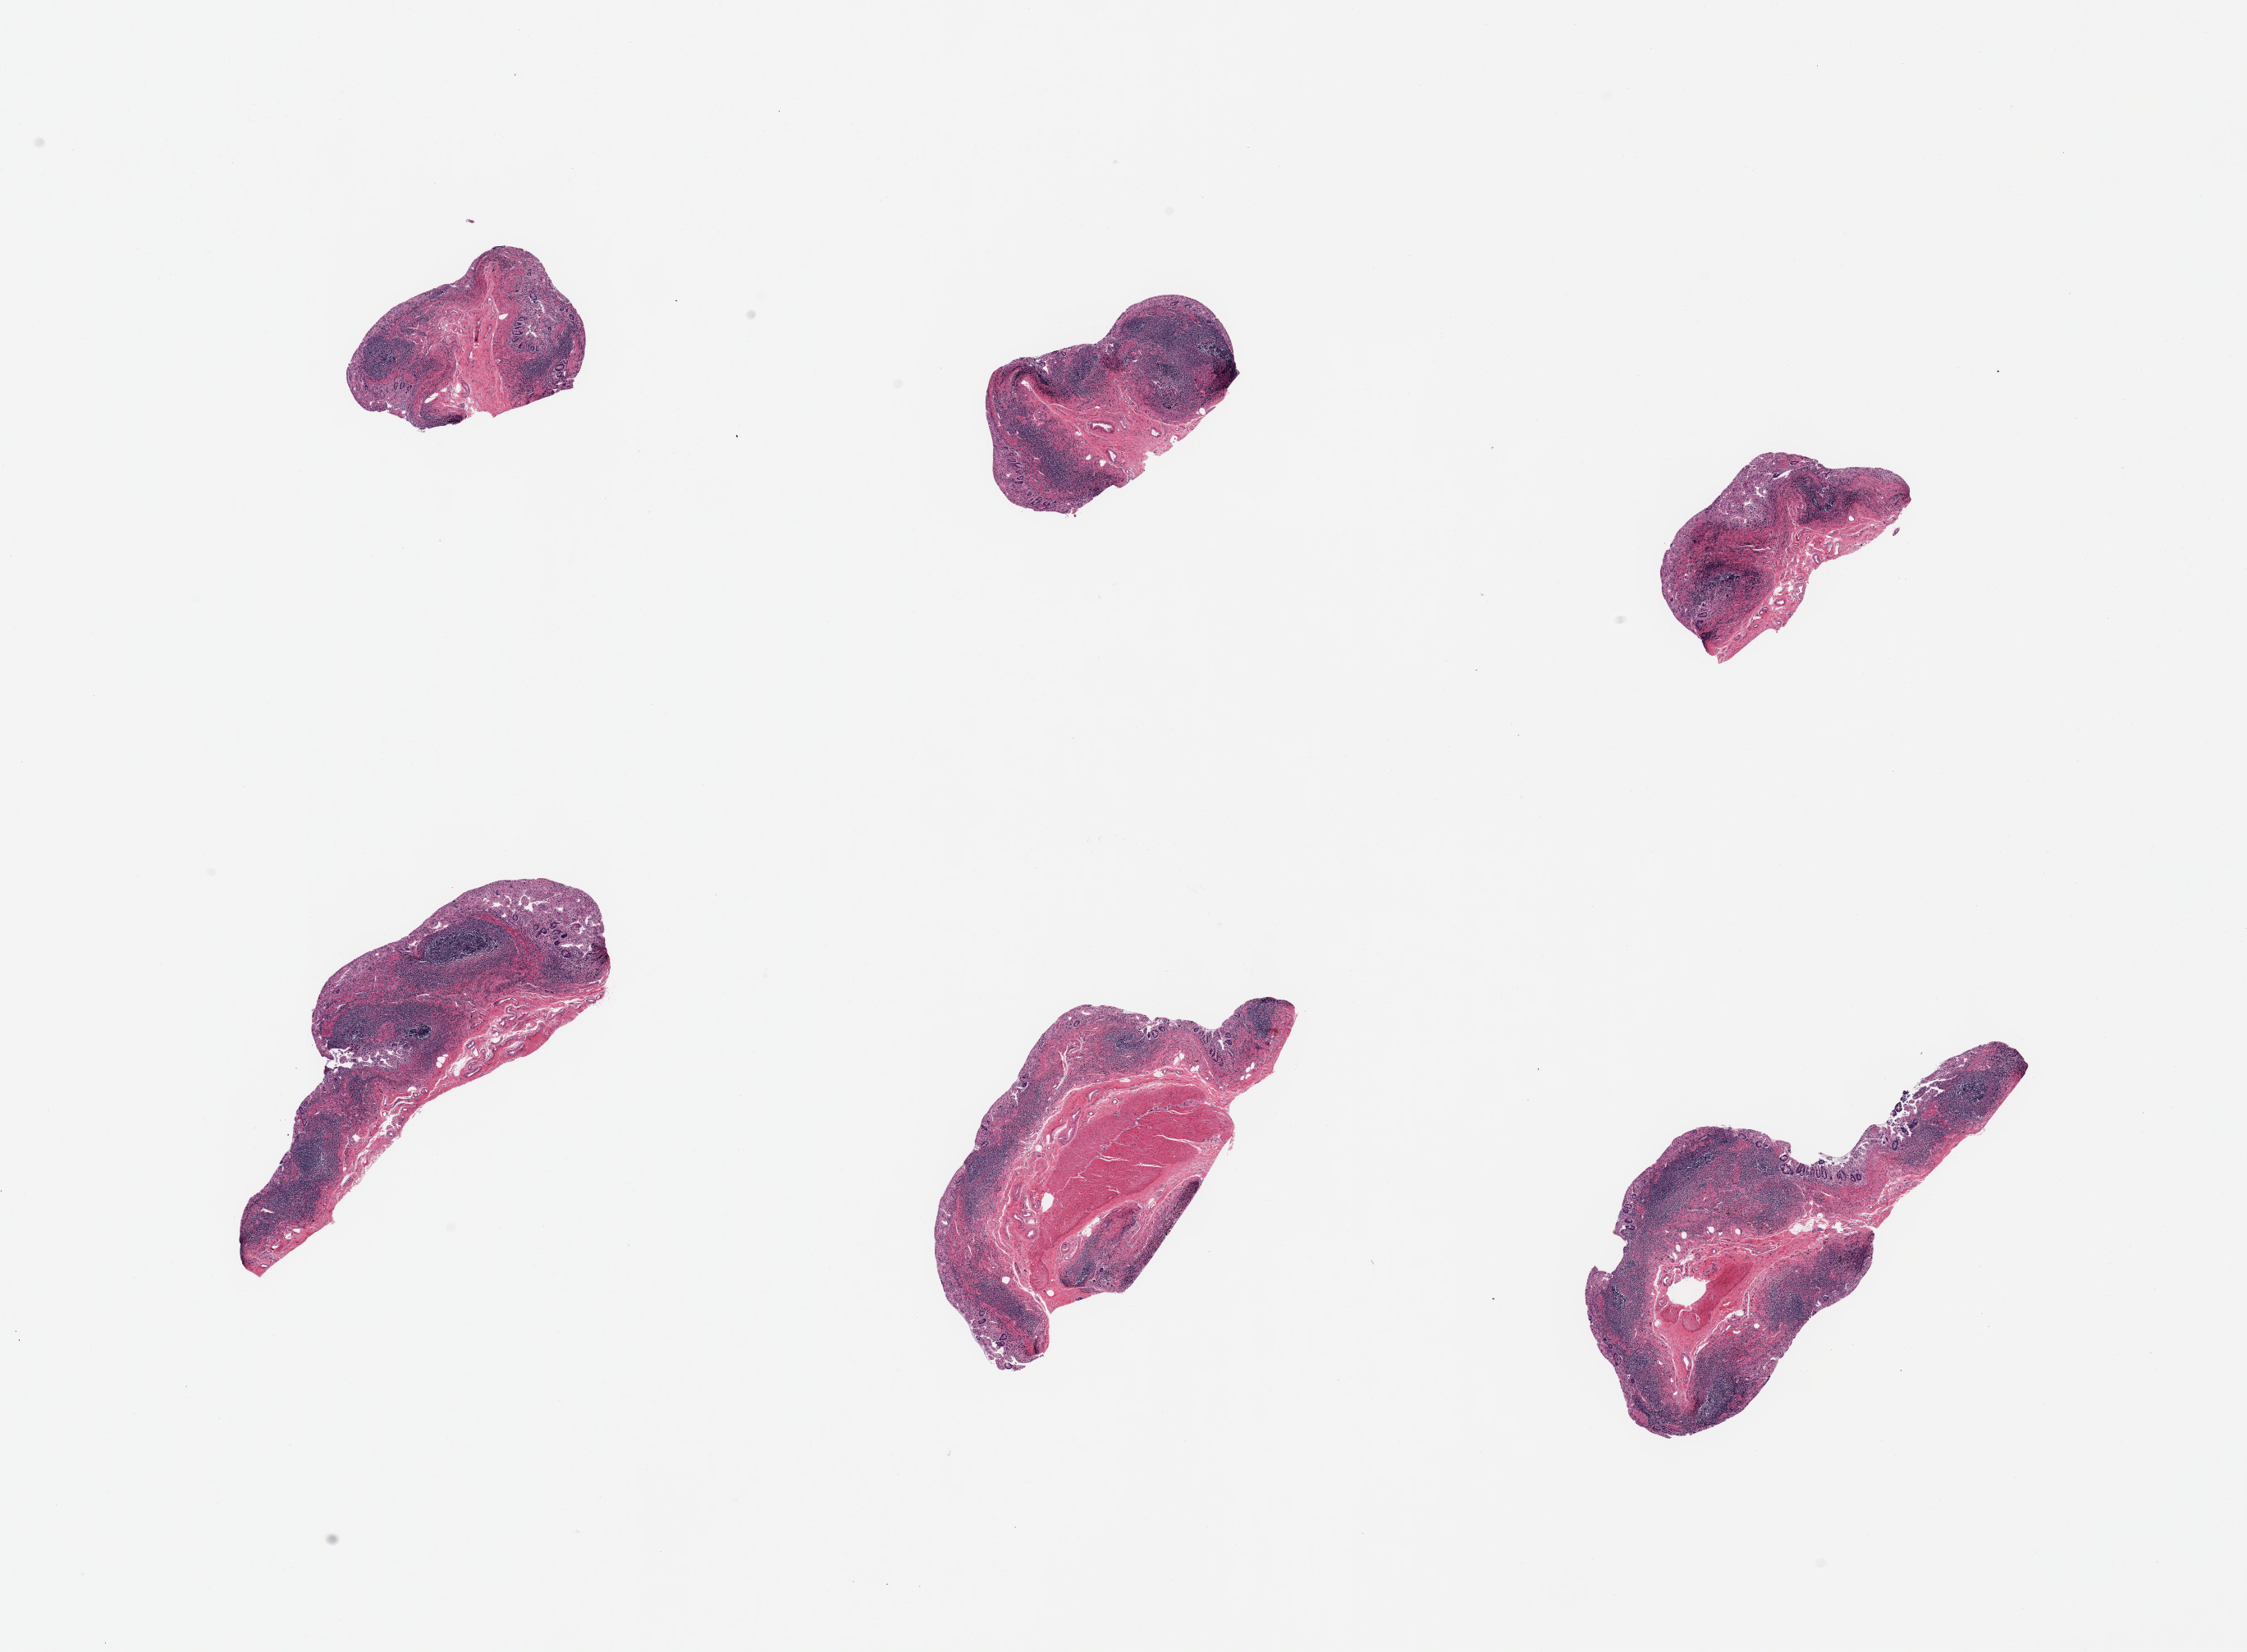
Whole-slide image, H&E stain, low-resolution overview of the scanned area, about 21.7 x 15.9 mm; PAXgene-fixed paraffin-embedded (PFPE) section; section of ileum (target tissue); tissue donor sample. Donor: male.
Review note (as recorded): 6 pieces; moderately to severely autolyzed mucosa and abundant lymphoid tissue.